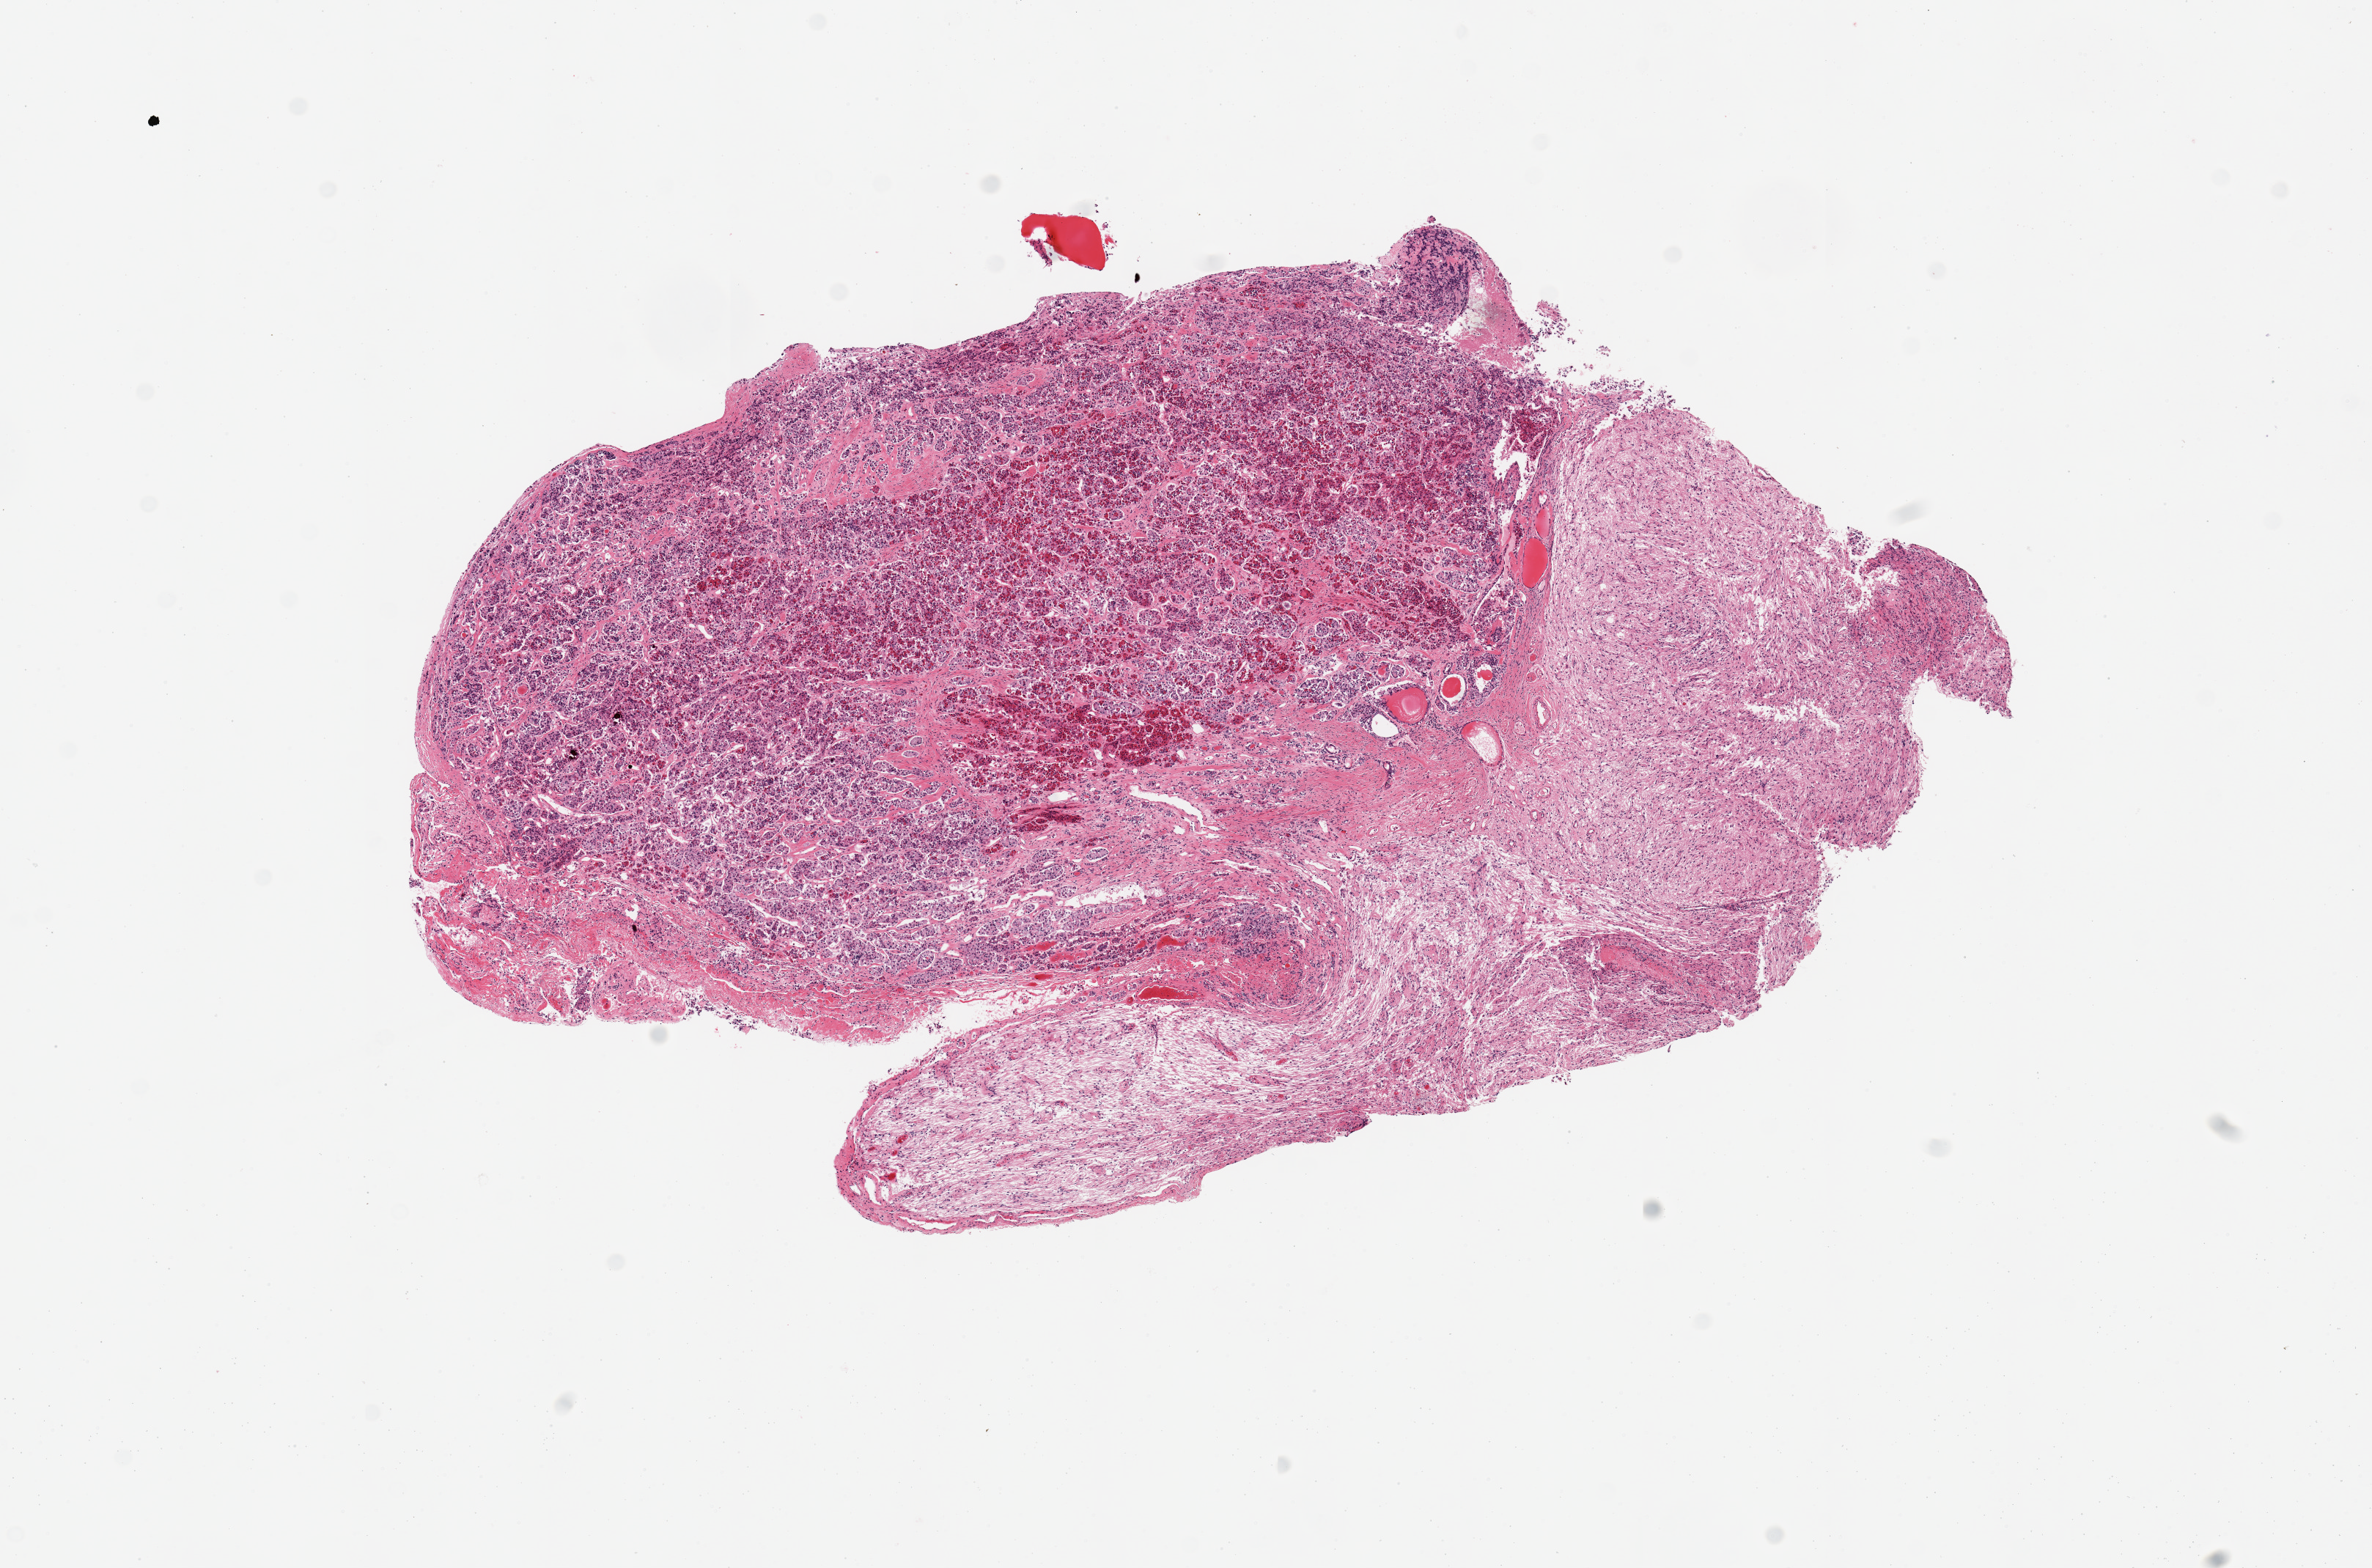
Digitized H&E-stained section, a low-resolution overview of the entire scanned area, about 12.8 x 8.5 mm (acquisition: 20x scan). PAXgene-fixed paraffin-embedded (PFPE) section. Section of pituitary (target tissue). Donor tissue sample. Donor sex: male.
* reviewer comment on this tissue sample: 2 pieces, ~40% neurohypophysis; rest is adenohypophysis